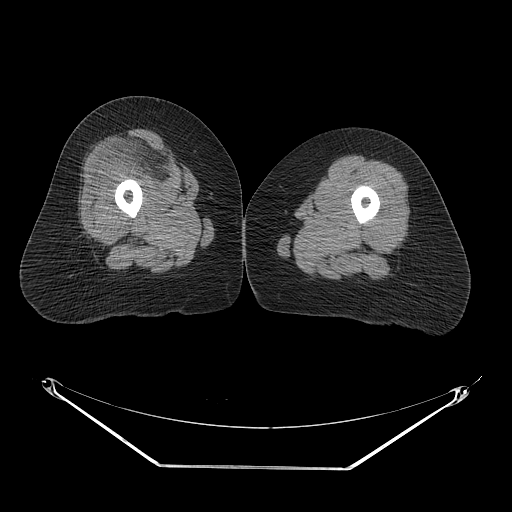
CT of an extremity soft-tissue mass (from a PET/CT study), one axial slice. Slice 23 of 267 in the series (ordered by position). Reconstruction kernel STANDARD. Soft-tissue window (W 400 / L 40 HU). 512 × 512 image matrix, field of view 500 × 500 mm. Female patient. From the clinical record (not read from this slice): histological type: malignant solitary fibrous tumor; grade: intermediate; site of the primary tumour: right thigh.
Outlined on this slice (expert contour drawn on MRI and transferred to this co-registered scan by the dataset authors):
- gross tumour volume including surrounding oedema: bounding box [x1, y1, x2, y2] px = [114, 130, 200, 197]
- gross tumour volume (mass): [146, 151, 172, 177]